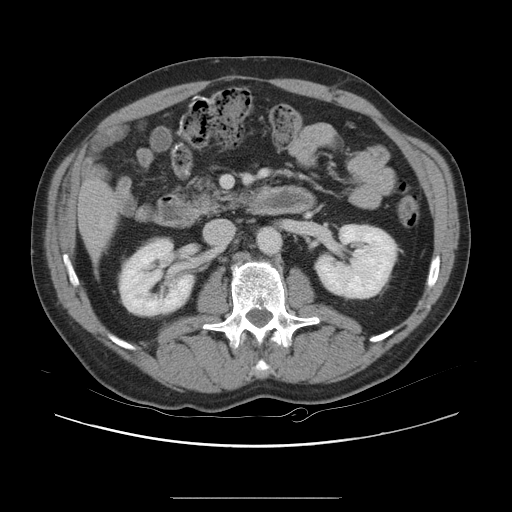
Contrast-enhanced abdominal CT, one axial slice. Position 5 of 40 along the scan axis. Intravenous contrast given. Soft-tissue window (W 400 / L 40 HU). 512 × 512 image matrix. Male patient, age 64 years. From the clinical record (not read from this slice): diagnosis: colorectal cancer liver metastases, imaged before liver resection; multiple liver metastases: yes; largest metastasis: 3.2 cm; disease in both lobes: yes.
Annotated regions visible in this slice (manually delineated by an expert):
- liver: bounding box [x1, y1, x2, y2] px = [80, 184, 116, 252]